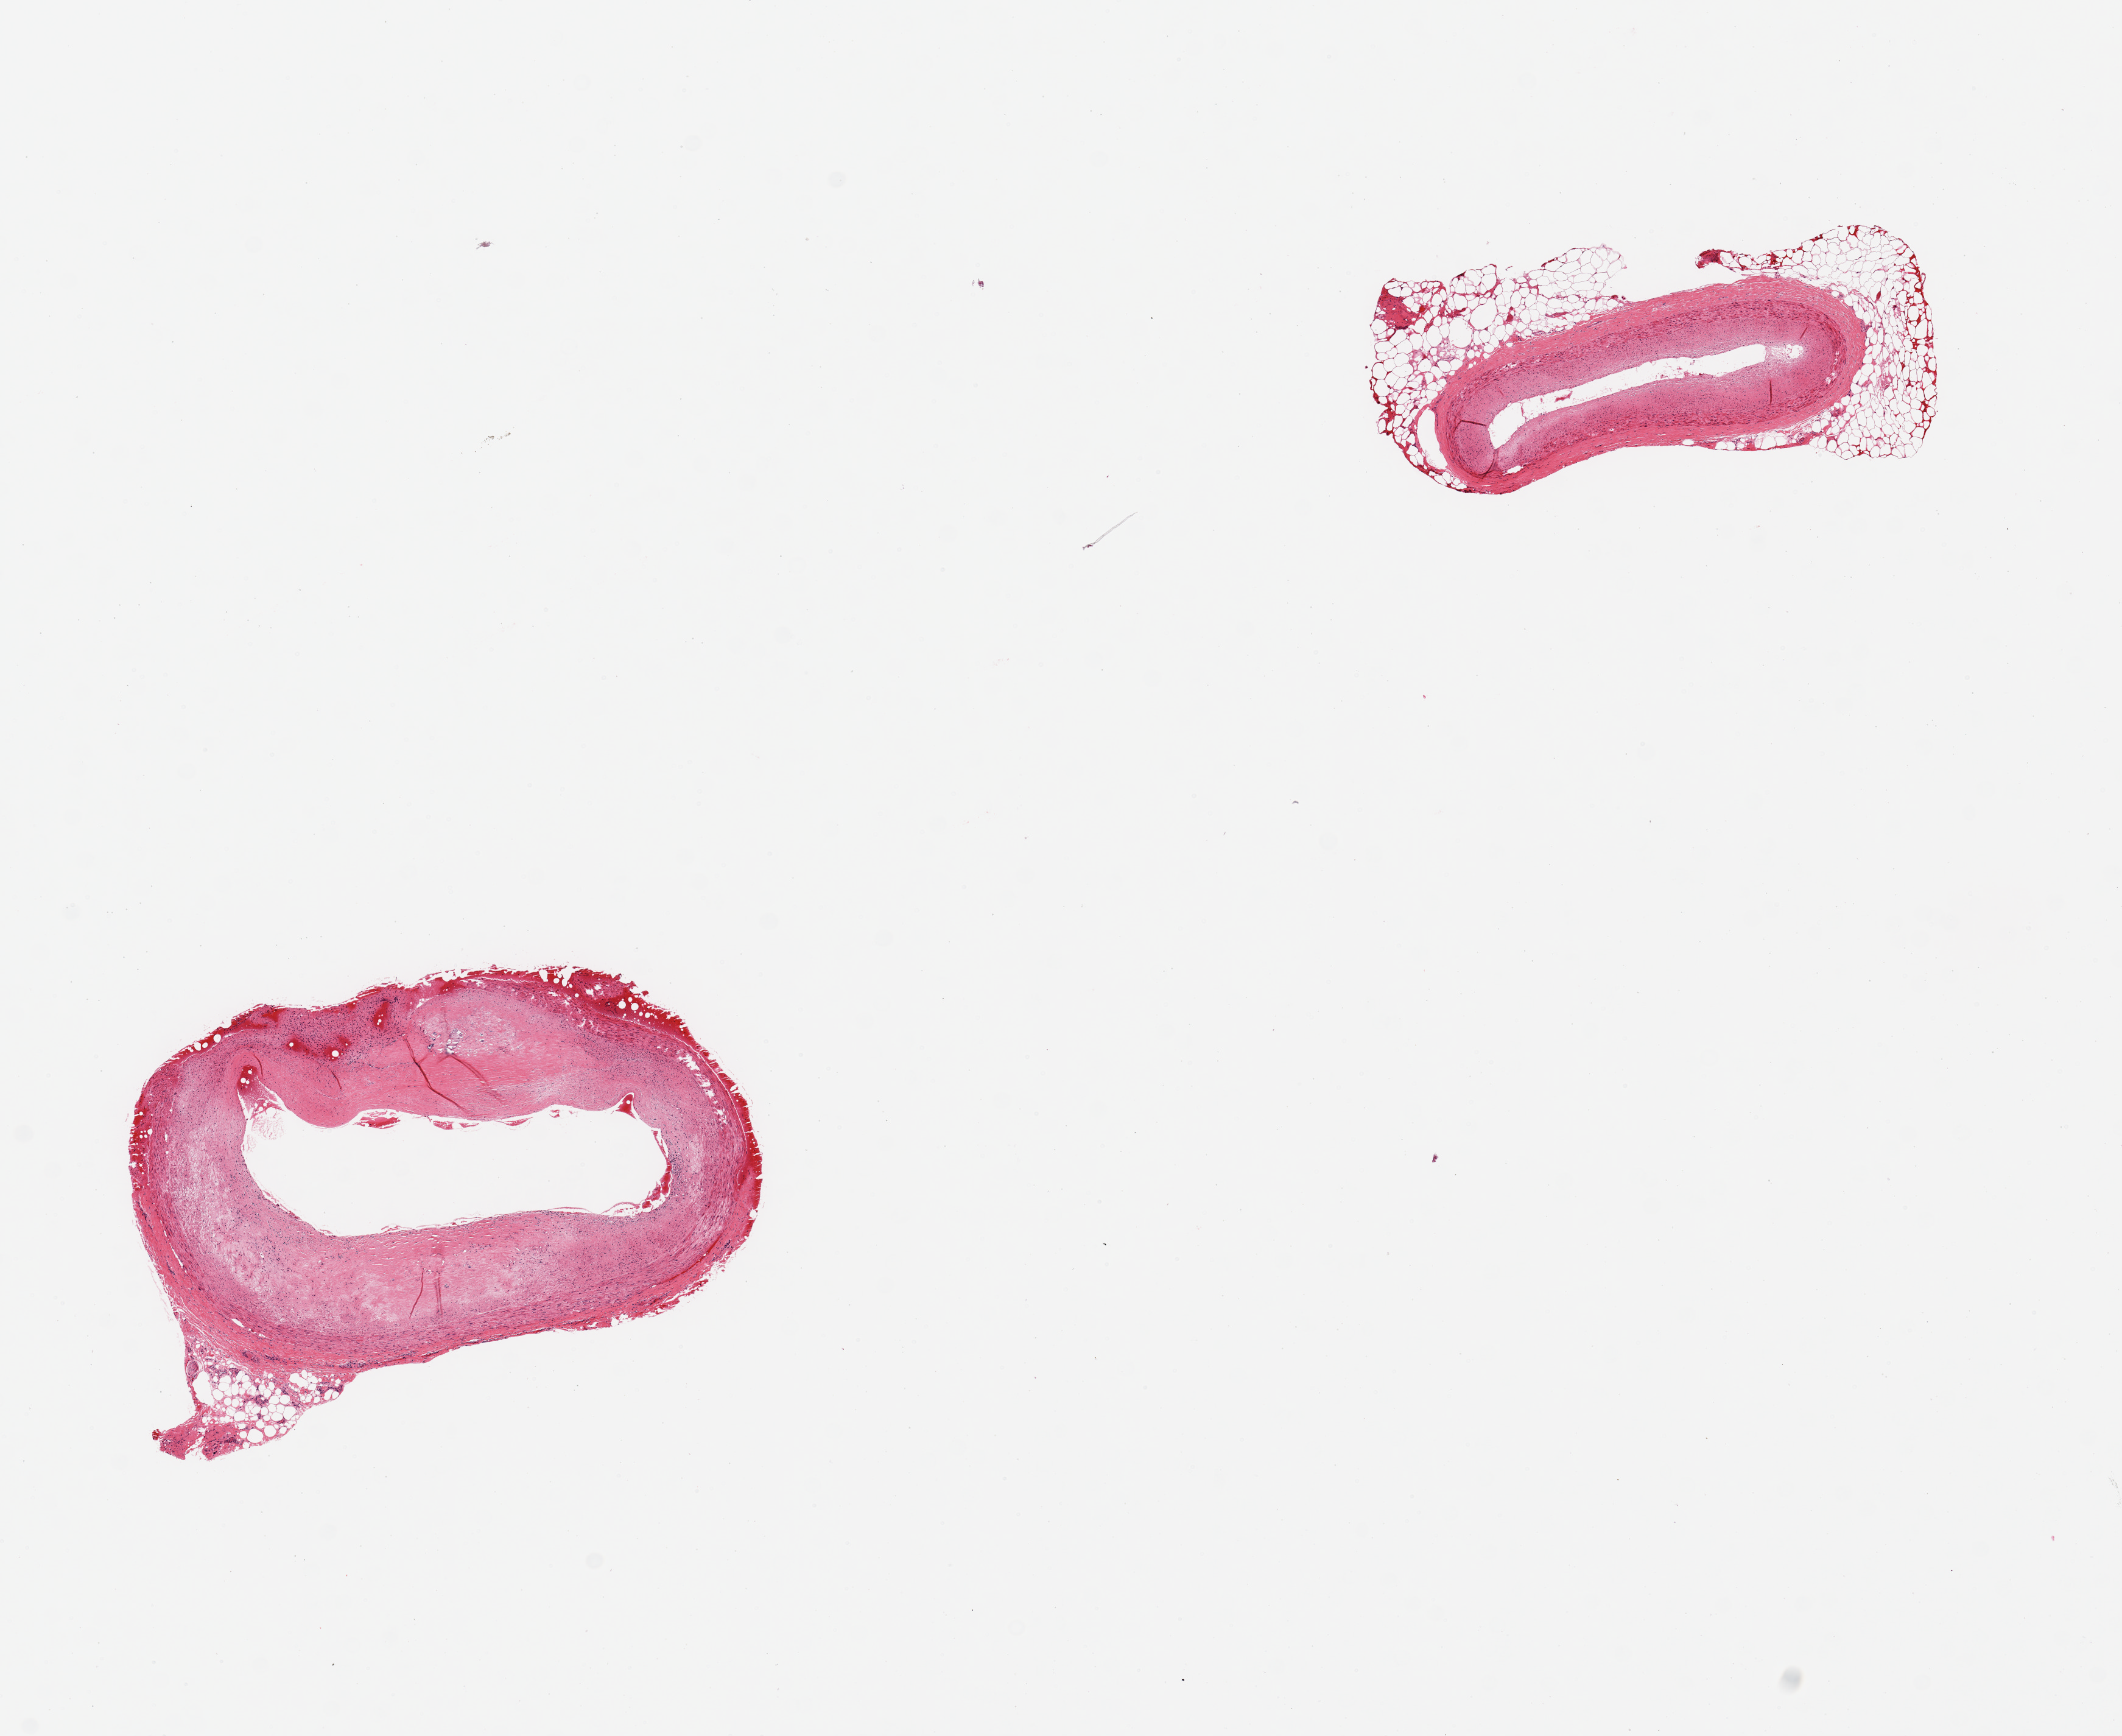
Hematoxylin and eosin (H&E) whole-slide image, whole scanned area (about 13.8 x 11.3 mm, from a 20x scan) shown as a low-resolution overview. PAXgene-fixed paraffin-embedded (PFPE) section. Section of coronary artery (target tissue). Donor tissue sample.
* review note (as recorded): 2 pieces, minimal atherosis, rim of discontinuous fat, ~0.5-0.8mm